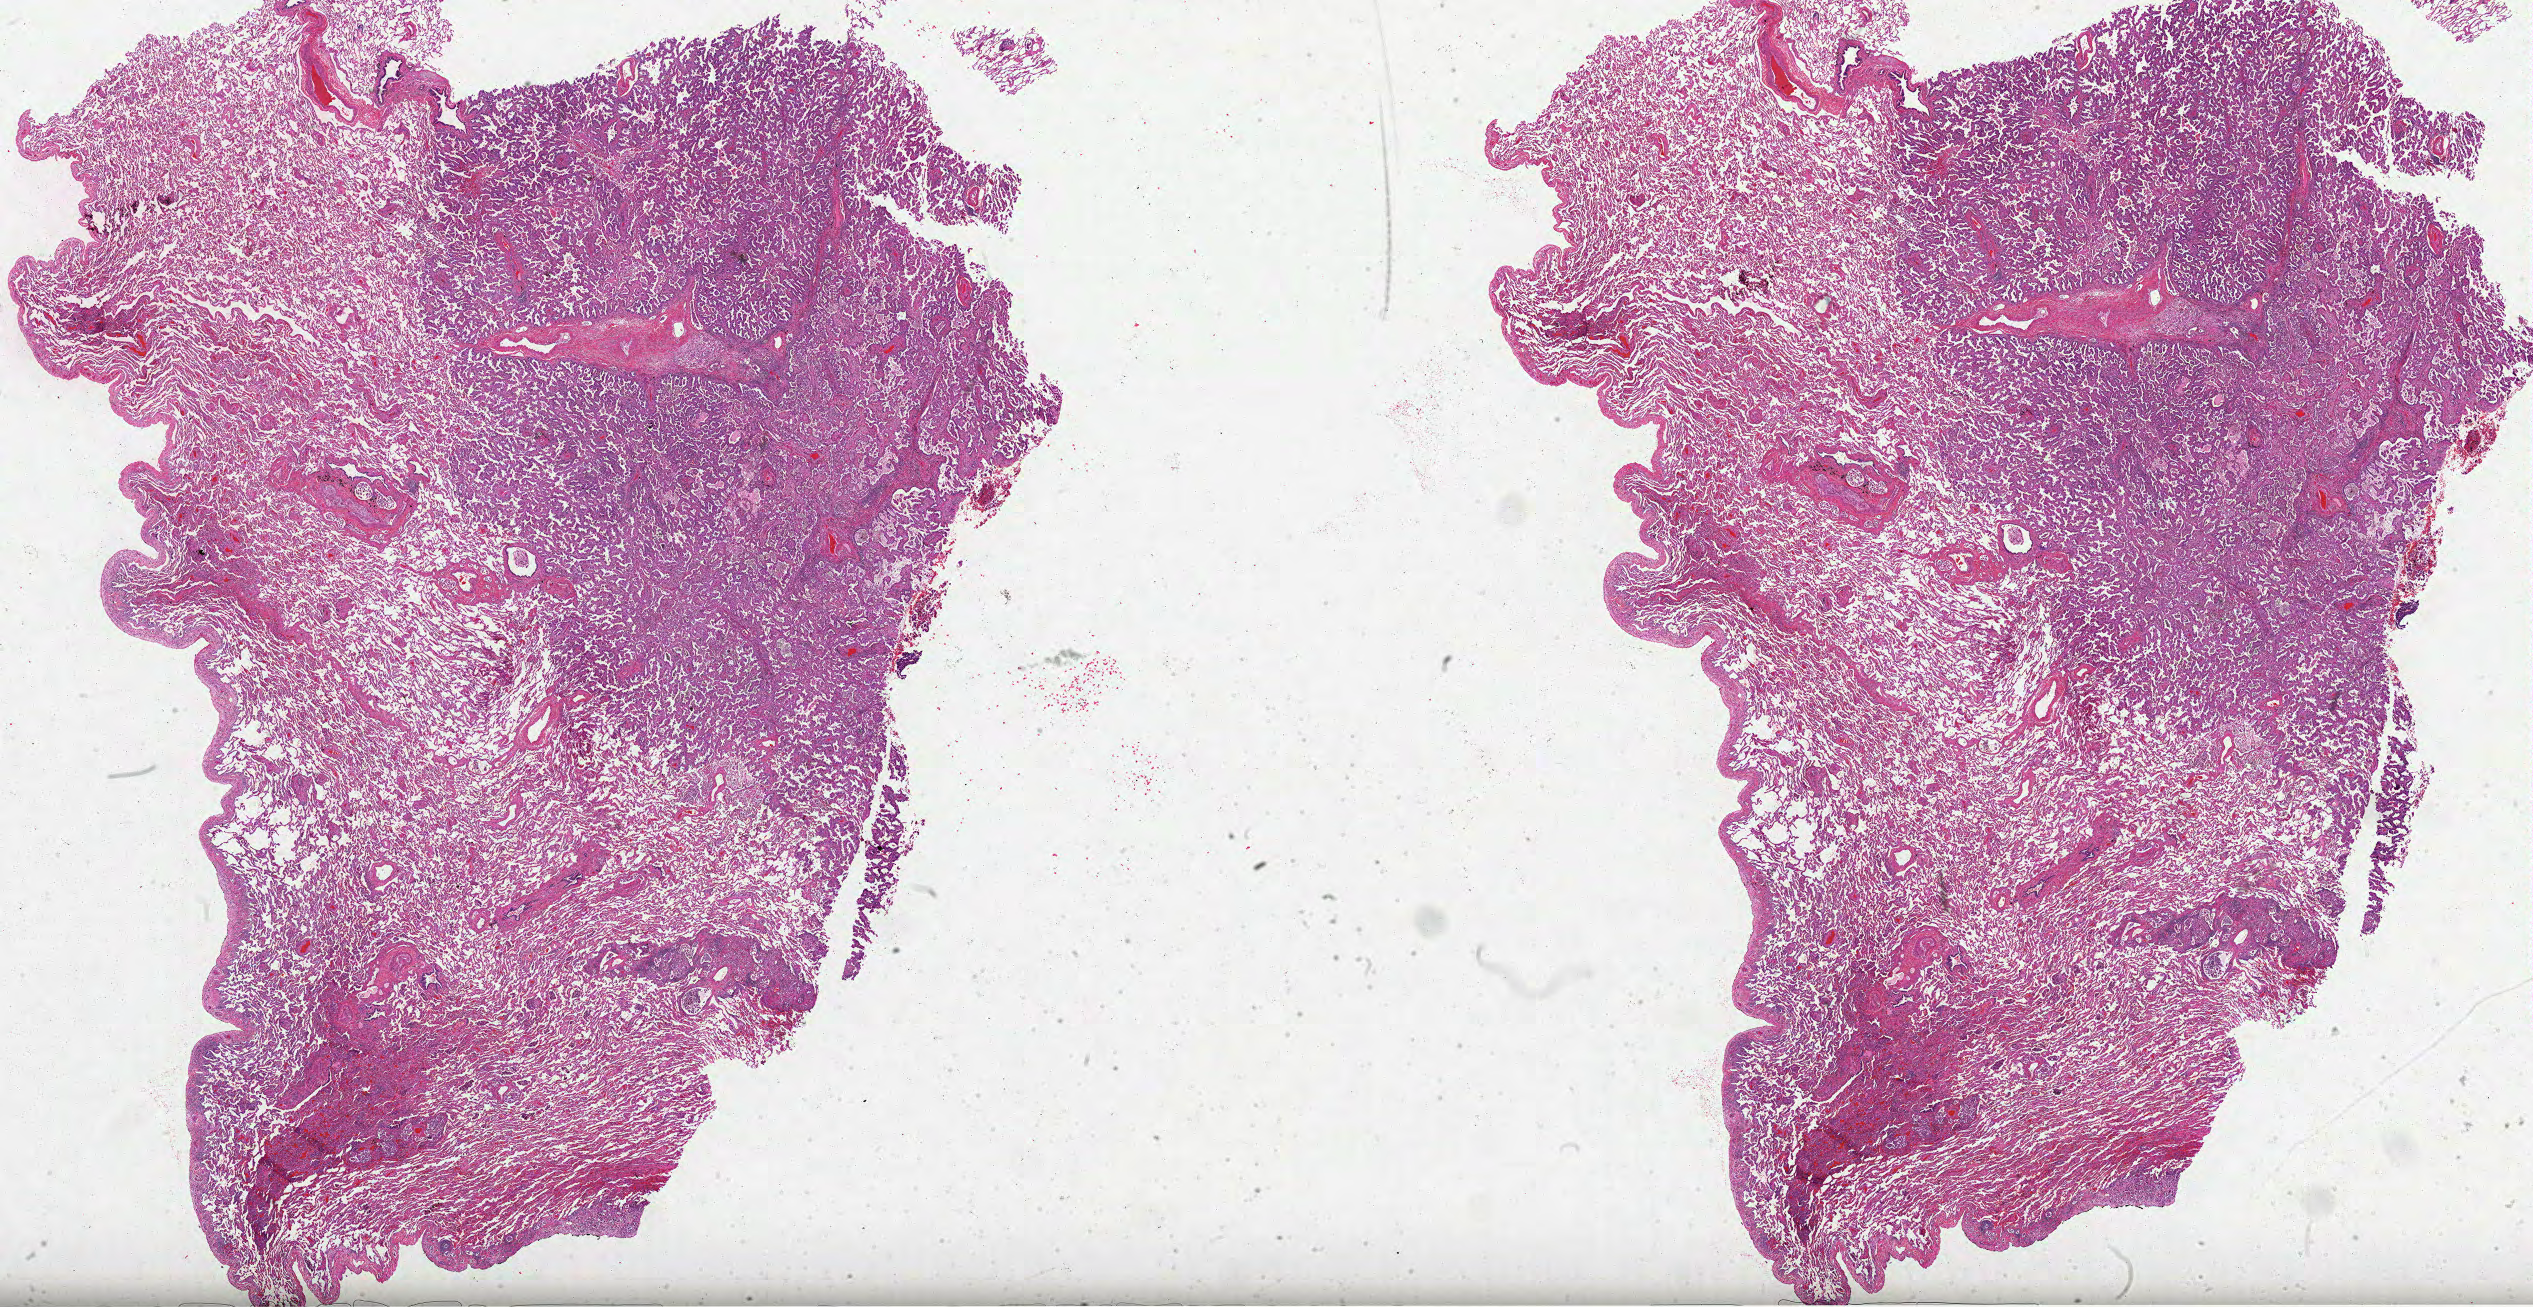
Whole-slide histology image, Hematoxylin and eosin (H&E) stained, low-resolution overview of the scanned area, about 40.9 x 21.1 mm (slide scanned at 40x), FFPE section, sample: primary tumour, lung. Patient: female, age at initial diagnosis 45 years.
* AJCC pathologic stage: IIIA
* diagnosis: Adenocarcinoma, NOS (upper lobe, lung)
* laterality: left